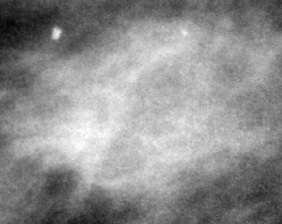
Cropped region of a digitized screen-film mammogram centred on a radiologist-marked abnormality, right breast, MLO view.
Marked abnormality: mass; BI-RADS assessment category 0 (incomplete: needs additional imaging); pathology result (as recorded, not read from the image): benign.